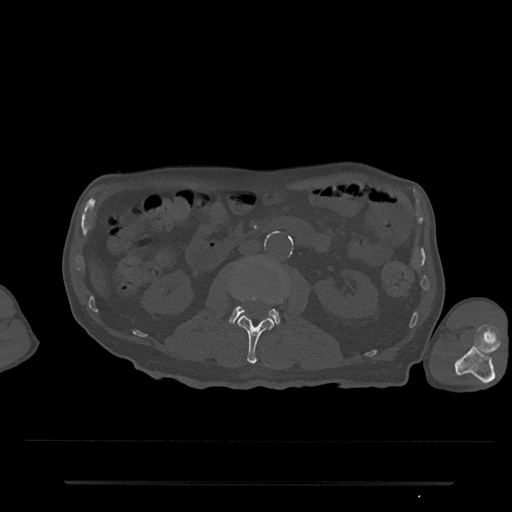
CT including the spine, one axial slice. Slice 32 of 797 in the series (ordered by position). Reconstruction kernel Br40s/3. Bone window (W 1800 / L 400 HU). 0.5 mm slice thickness. 512 × 512 image matrix. Male patient, age 74 years. From the clinical record (not read from this slice): primary cancer: prostate.
Structures marked on this image (semi-automatically segmented with operator editing):
- L2 vertebra: box from (x=238, y=295) to (x=283, y=364) px
- L3 vertebra: (x=228, y=306)–(x=280, y=325)